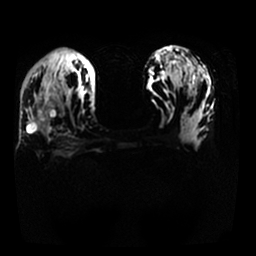
Breast MRI, one axial slice; position 16 of 25 along the scan axis; diffusion-weighted series; image 2 of 4 stored at this slice position (different b-values; order by instance number); 1.5 T; 4 mm slice thickness; 256 × 256 image matrix, field of view 340 × 340 mm. Female patient.
Outlined on this slice (manually delineated by an expert):
- tumour on diffusion-weighted imaging: bounding box (x1, y1, x2, y2) in pixels: (28, 97, 55, 129)